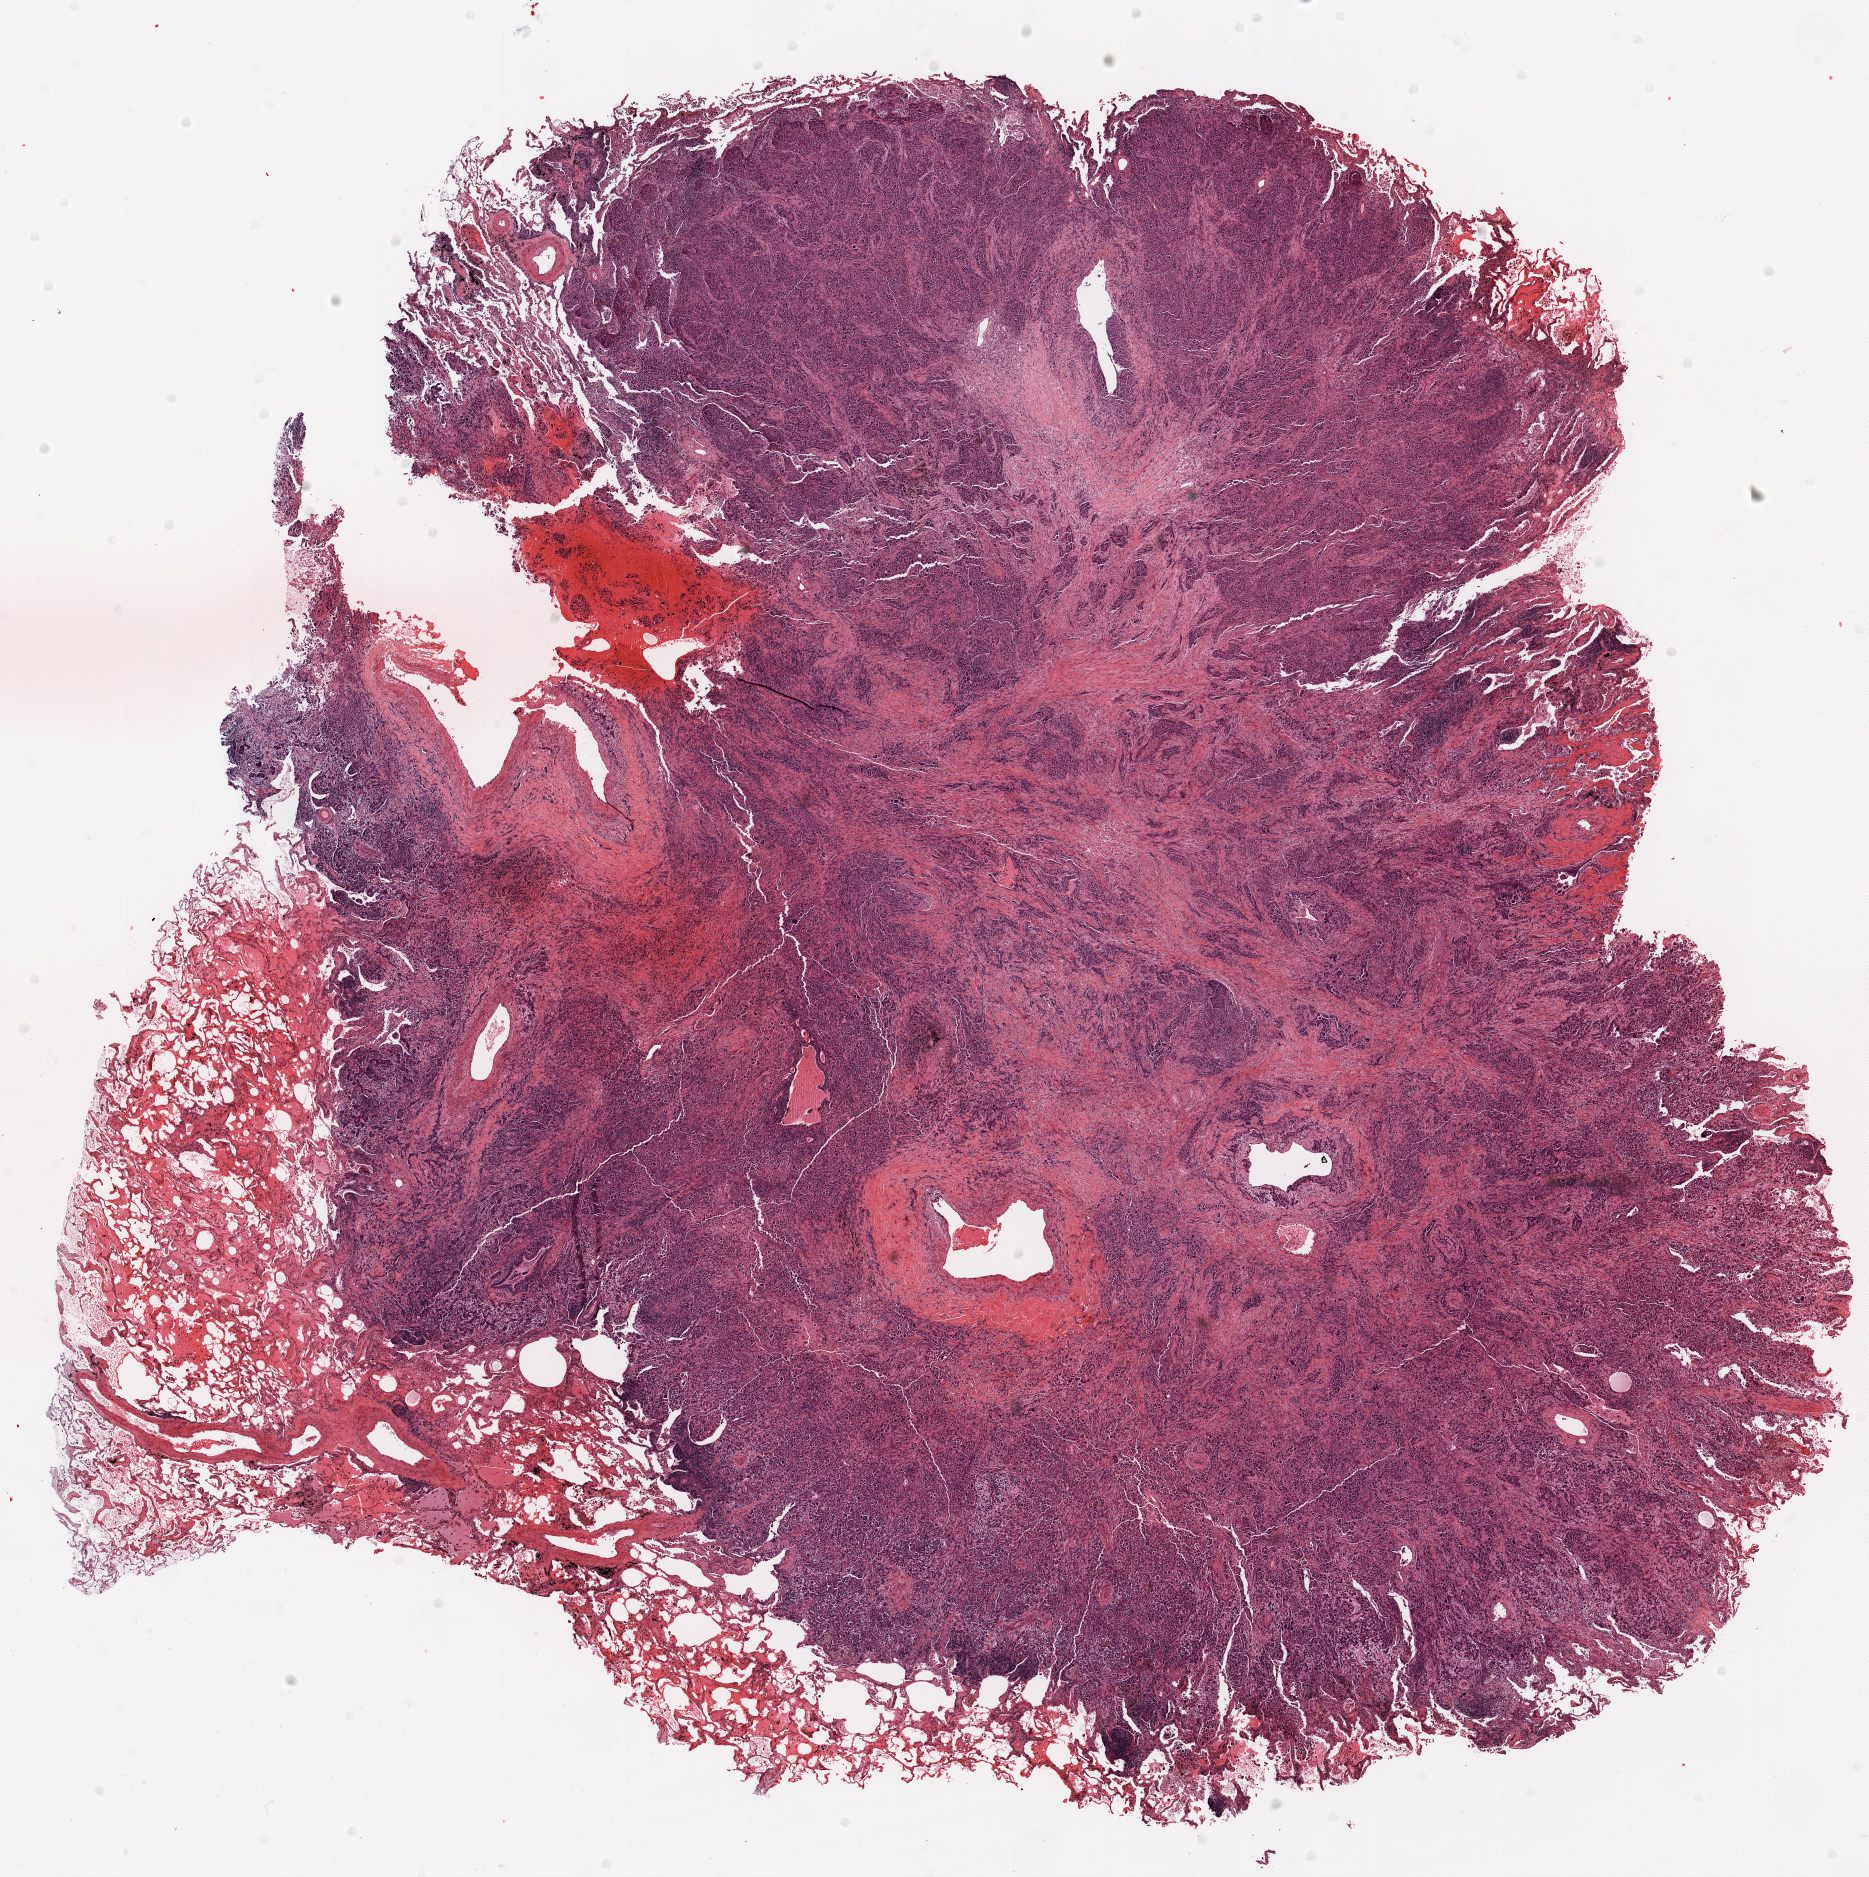
Whole-slide histology image, H&E, shown as a low-resolution overview of the whole scanned area (about 15.0 x 15.1 mm, from a 20x scan); FFPE section; lung tissue. Male, age 64 at enrolment. Current smoker at enrolment. Grade: poorly differentiated (G3).
Stage (AJCC 6th edition): IA. Participant's lung-cancer diagnosis: Adenocarcinoma, NOS. ICD-O-3 topography: upper lobe of lung (C34.1). Tumour size (pathology): 15 mm. Primary tumour location (clinical record): left upper lobe.